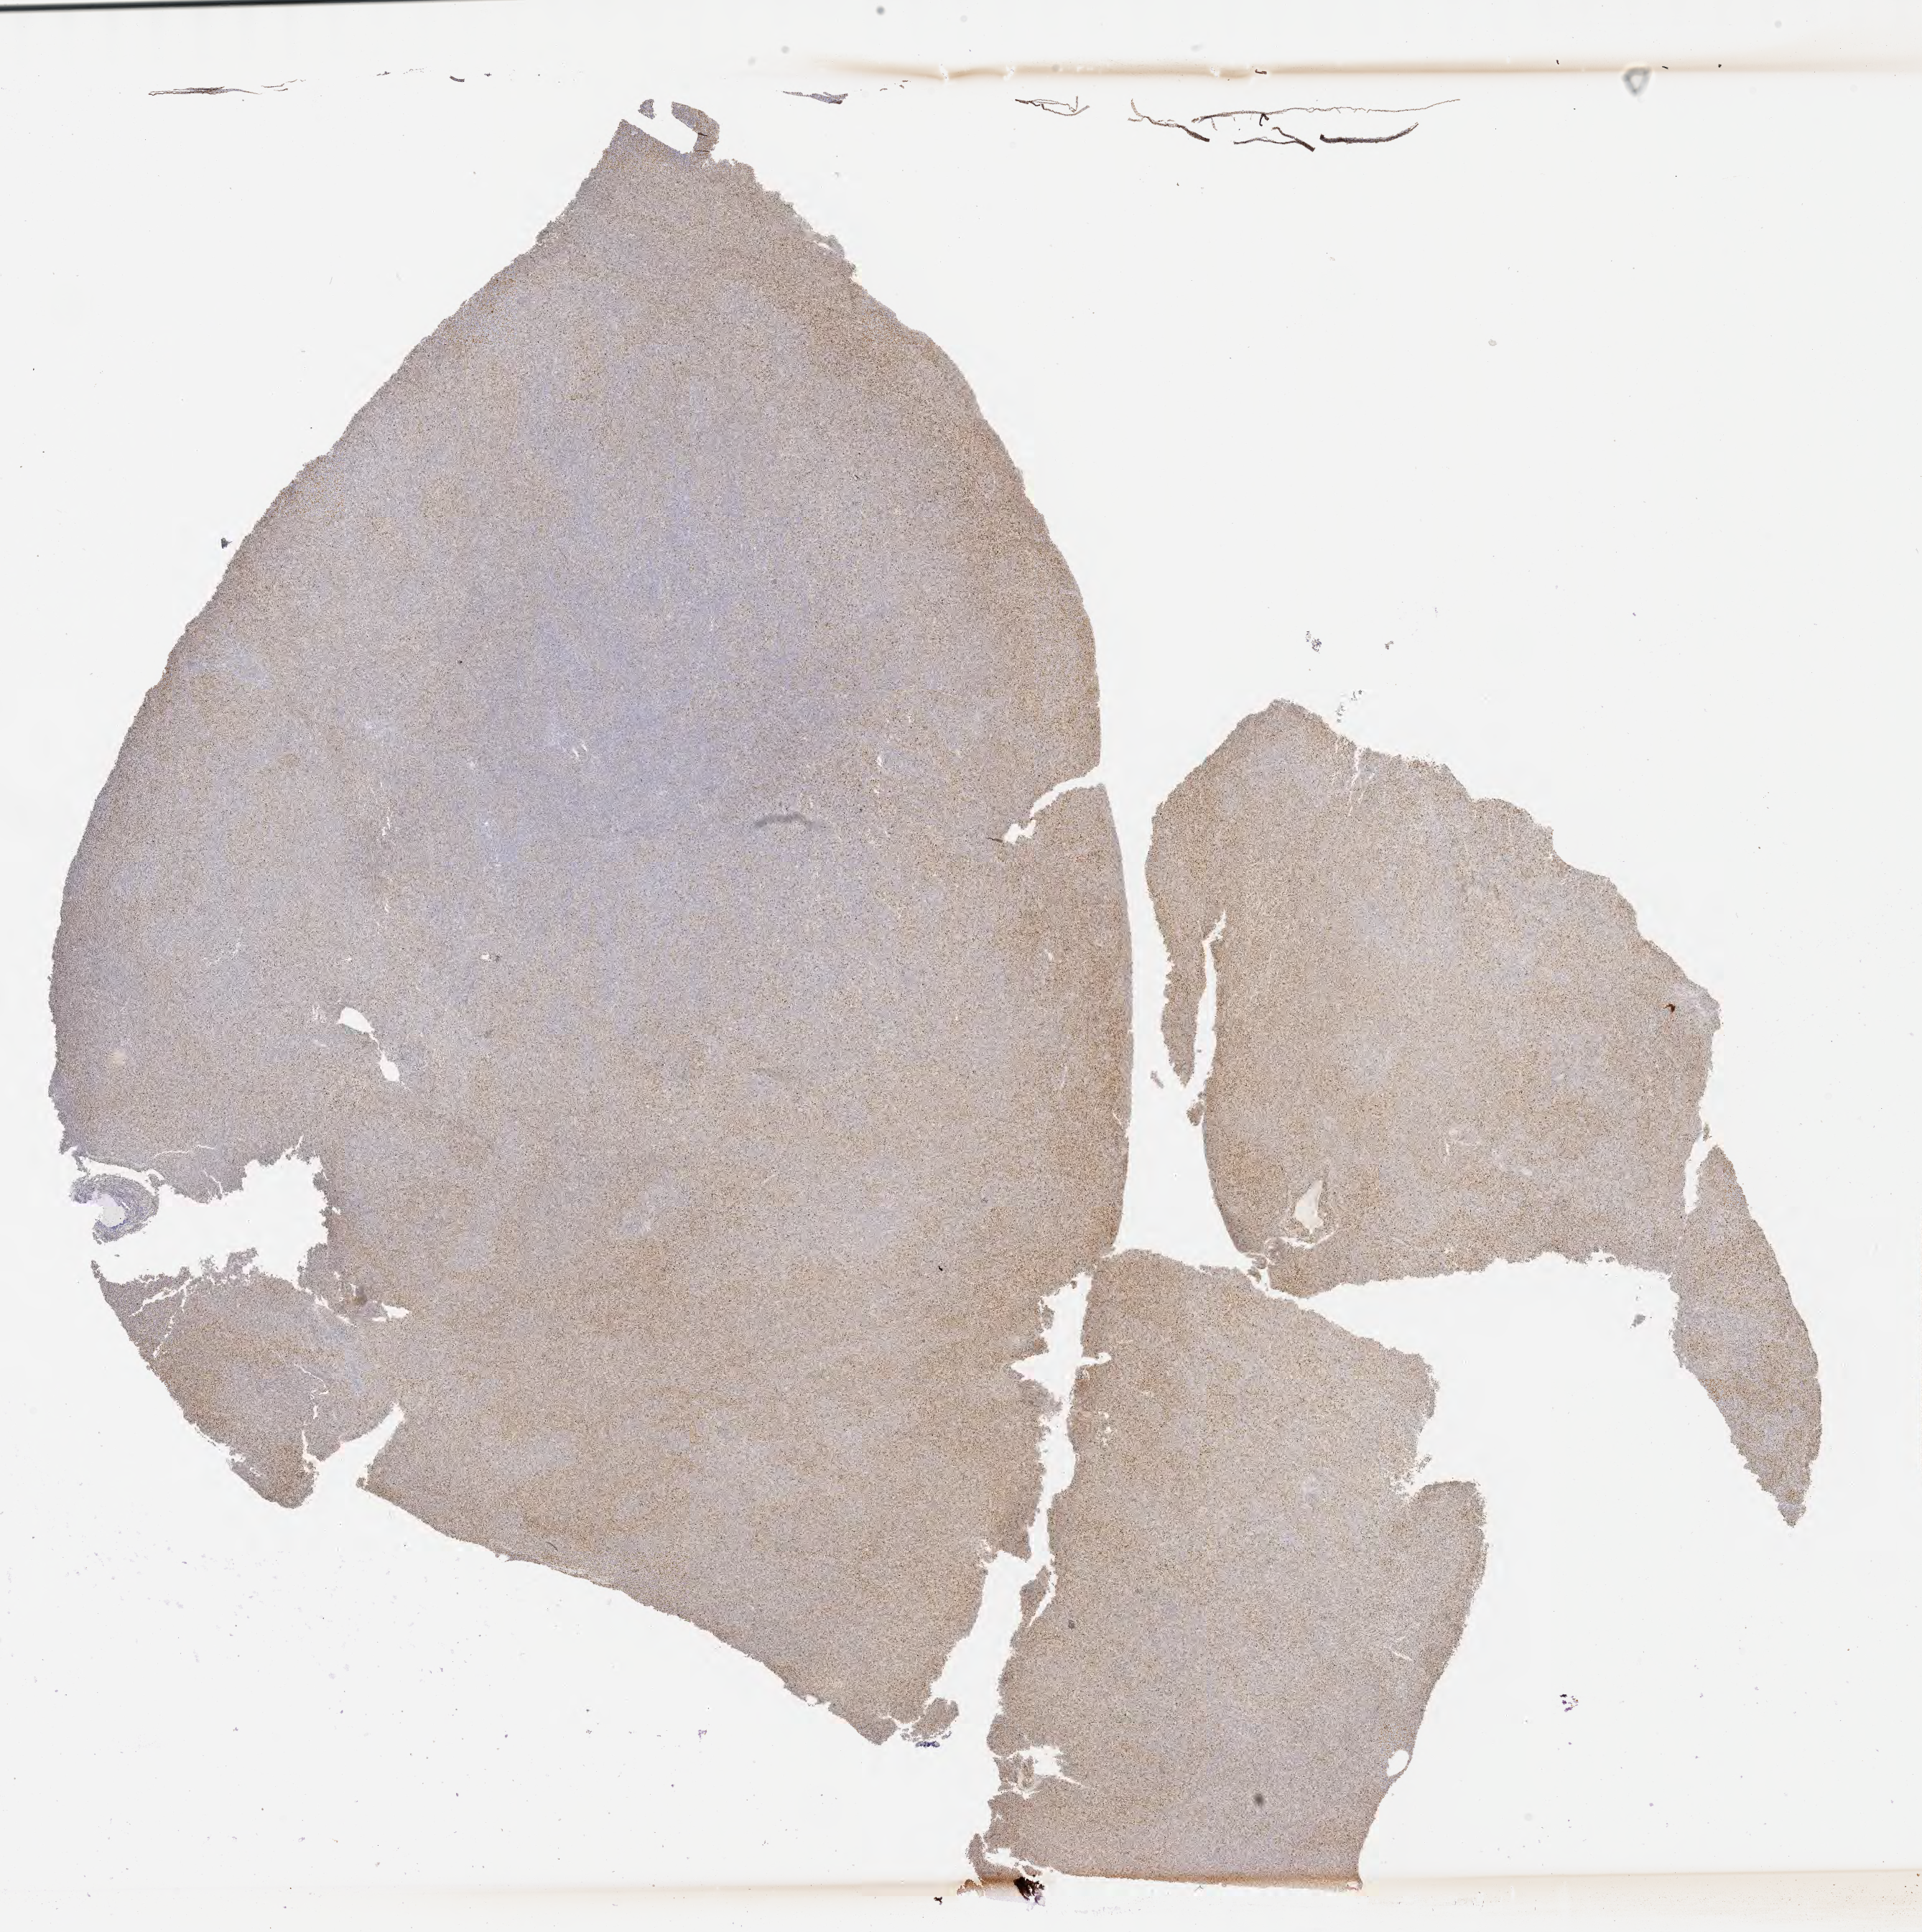
IHC for p53, whole-slide image, shown as a low-resolution overview of the whole scanned area (about 21.6 x 21.7 mm), tumor tissue, site: liver. Patient: female, aged 46.
Histologic diagnosis: Diffuse large B-cell lymphoma, NOS.